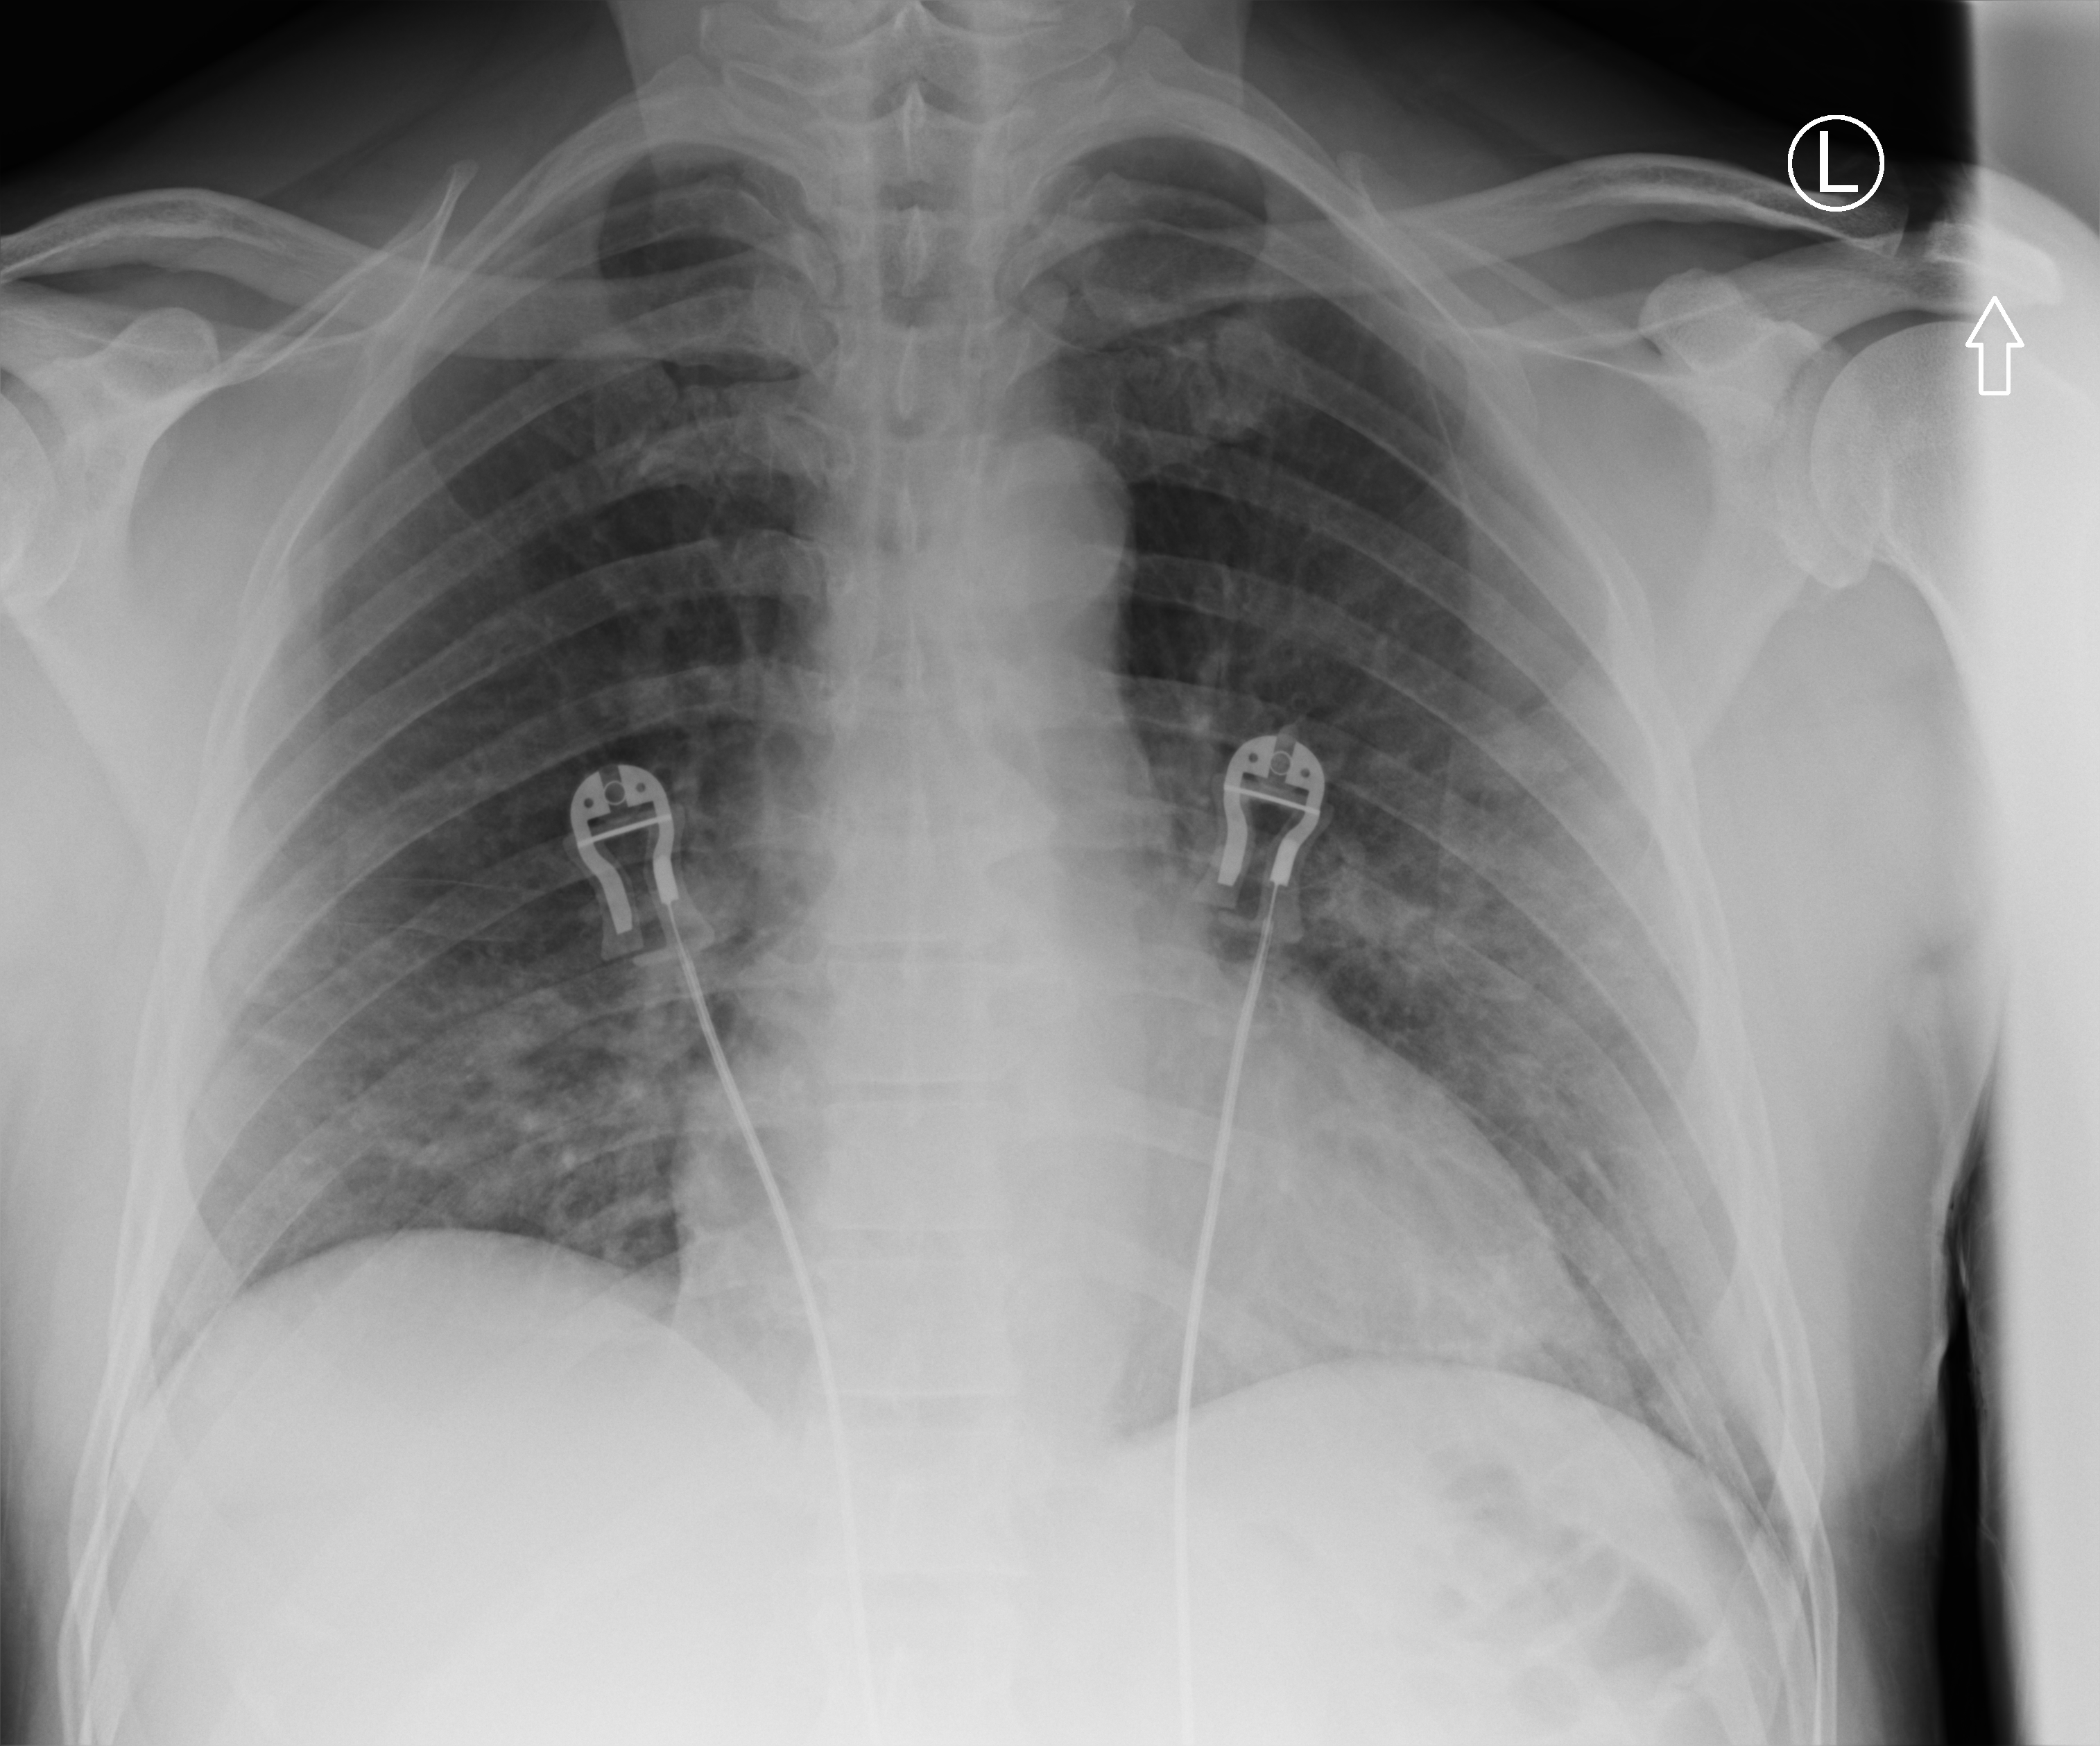
Chest X-ray (portable). Male patient hospitalised with COVID-19, age 18–59 years.
Hospital-stay facts (about this admission, not read from this image; timing relative to this image not recorded):
- length of hospital stay: 1 day
- mechanically ventilated during this hospital stay: no